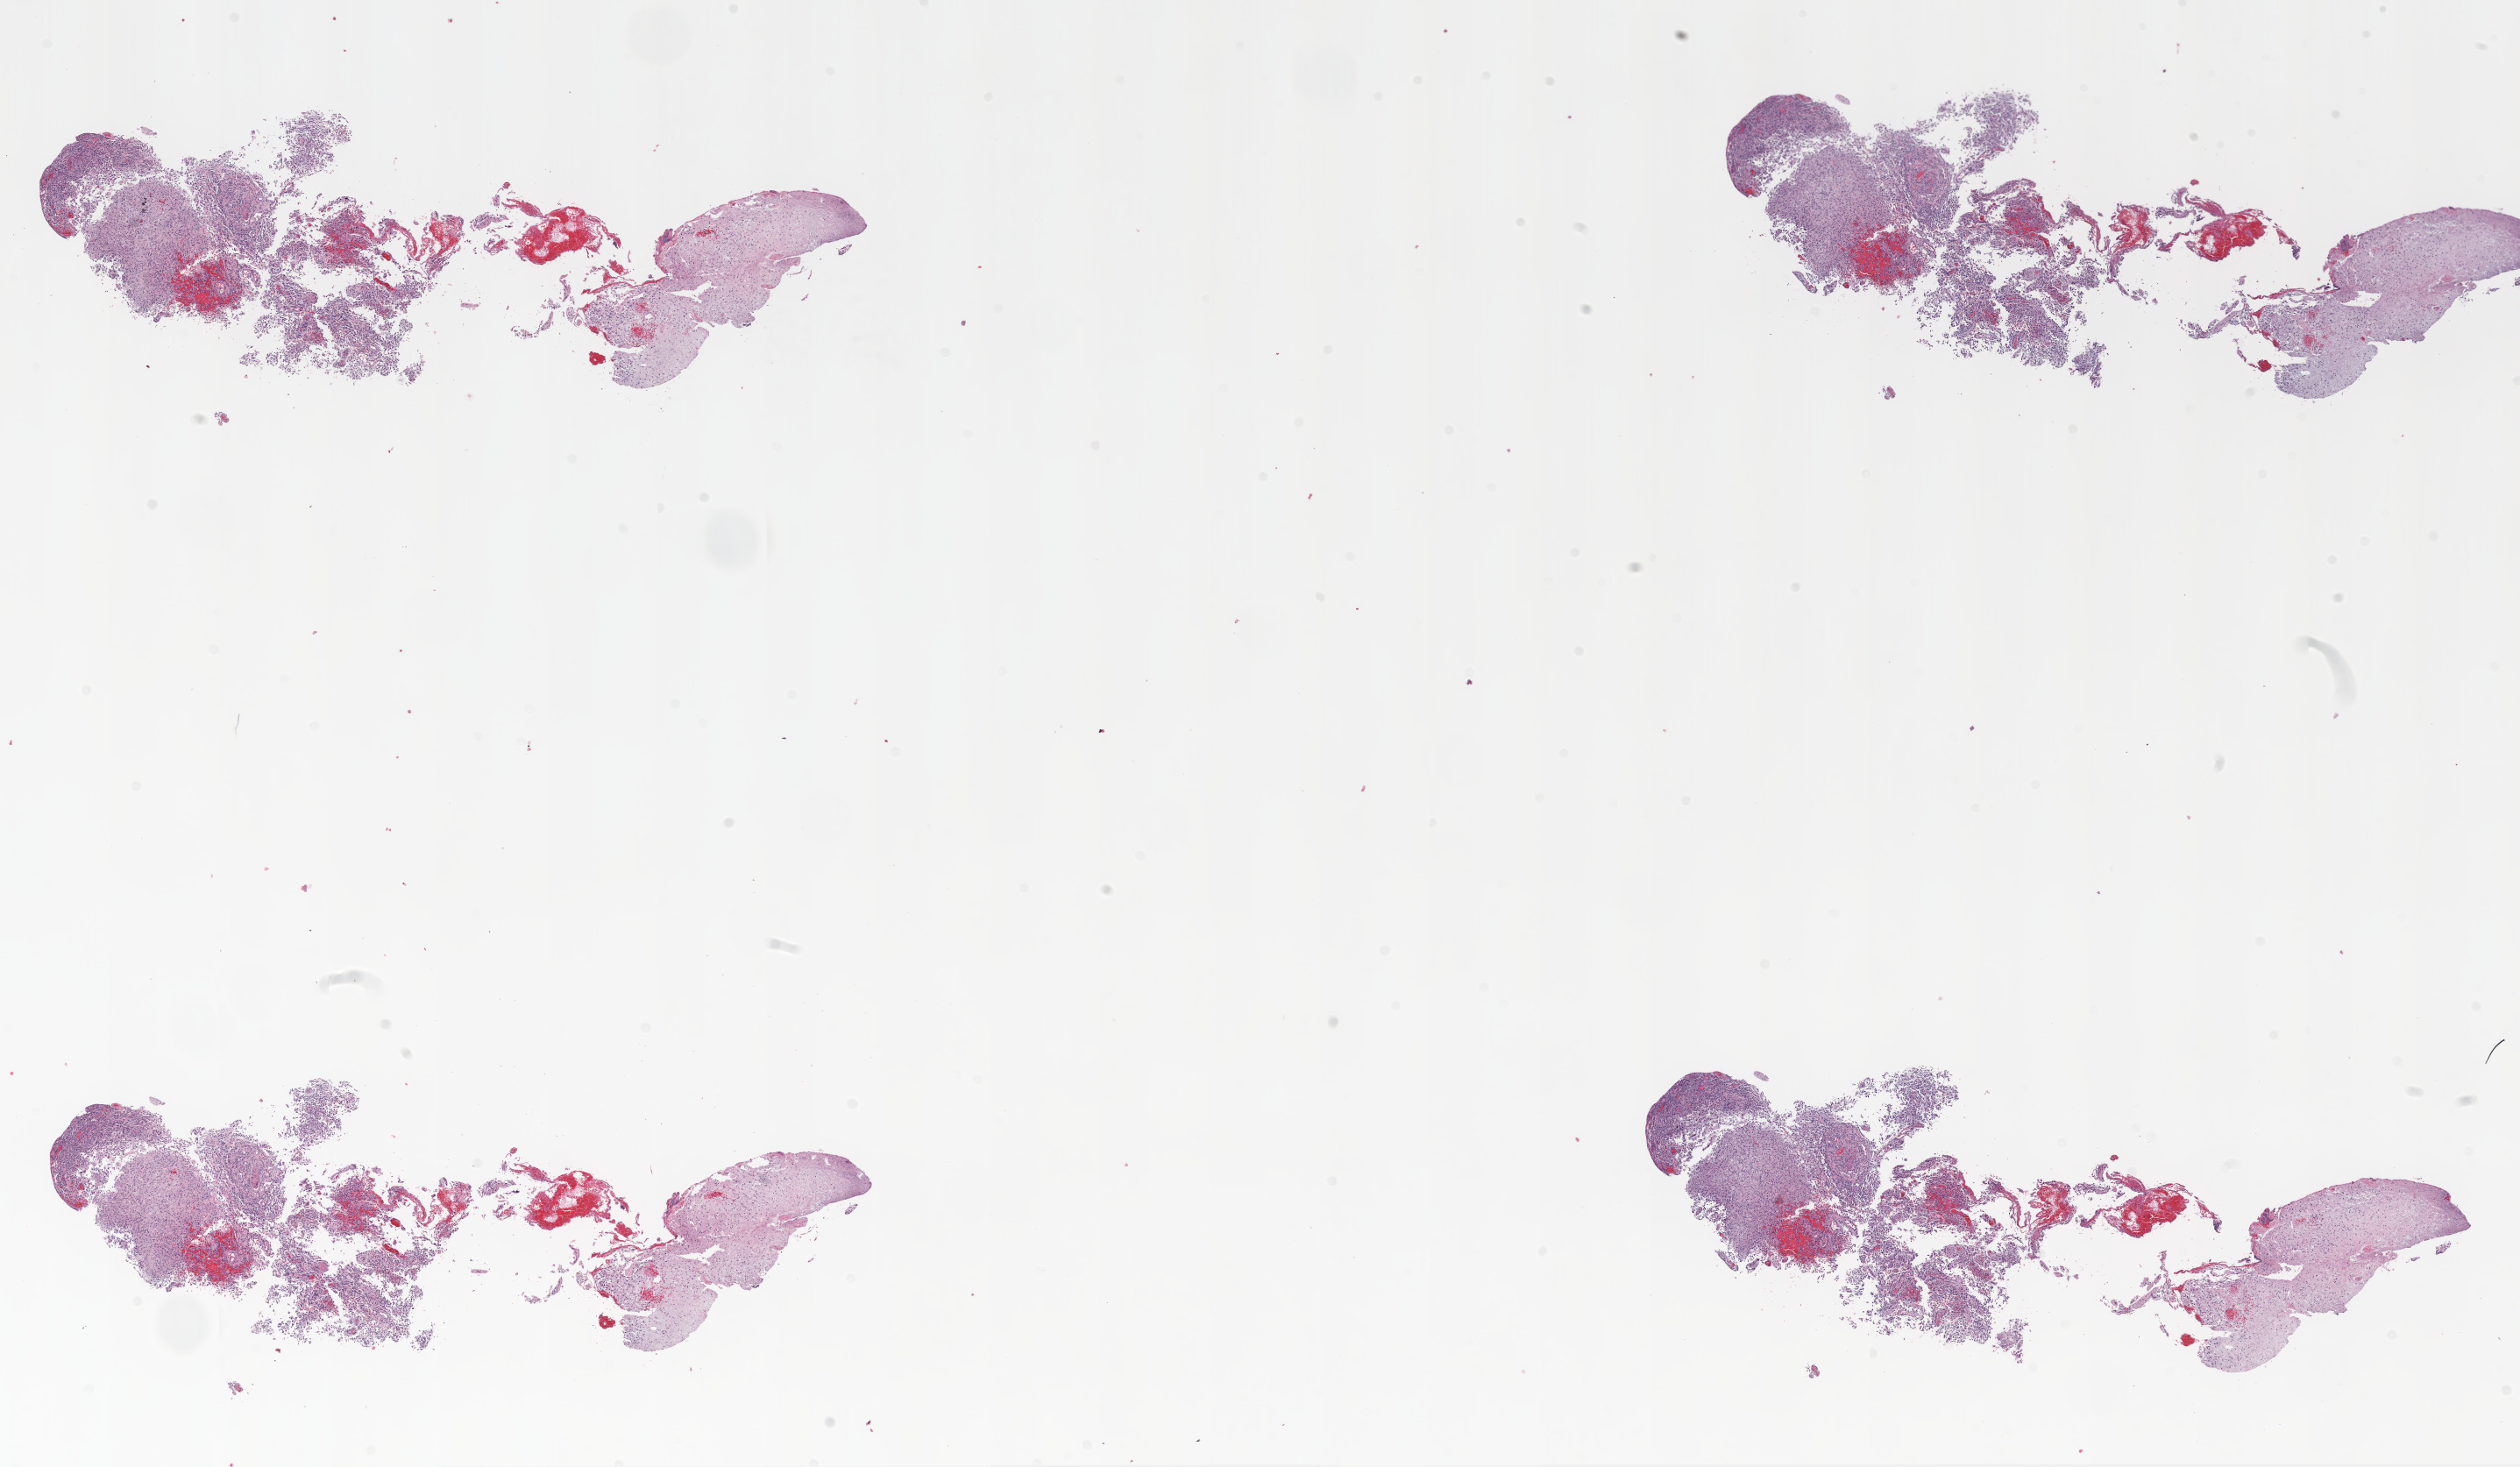
H&E whole-slide image, low-resolution overview of the scanned area, about 23.1 x 13.4 mm (slide scanned at 20x), formalin-fixed paraffin-embedded (FFPE) diagnostic section, brain, primary tumour sample. Patient: male, age at initial diagnosis 50 years.
Diagnosis: Glioblastoma.